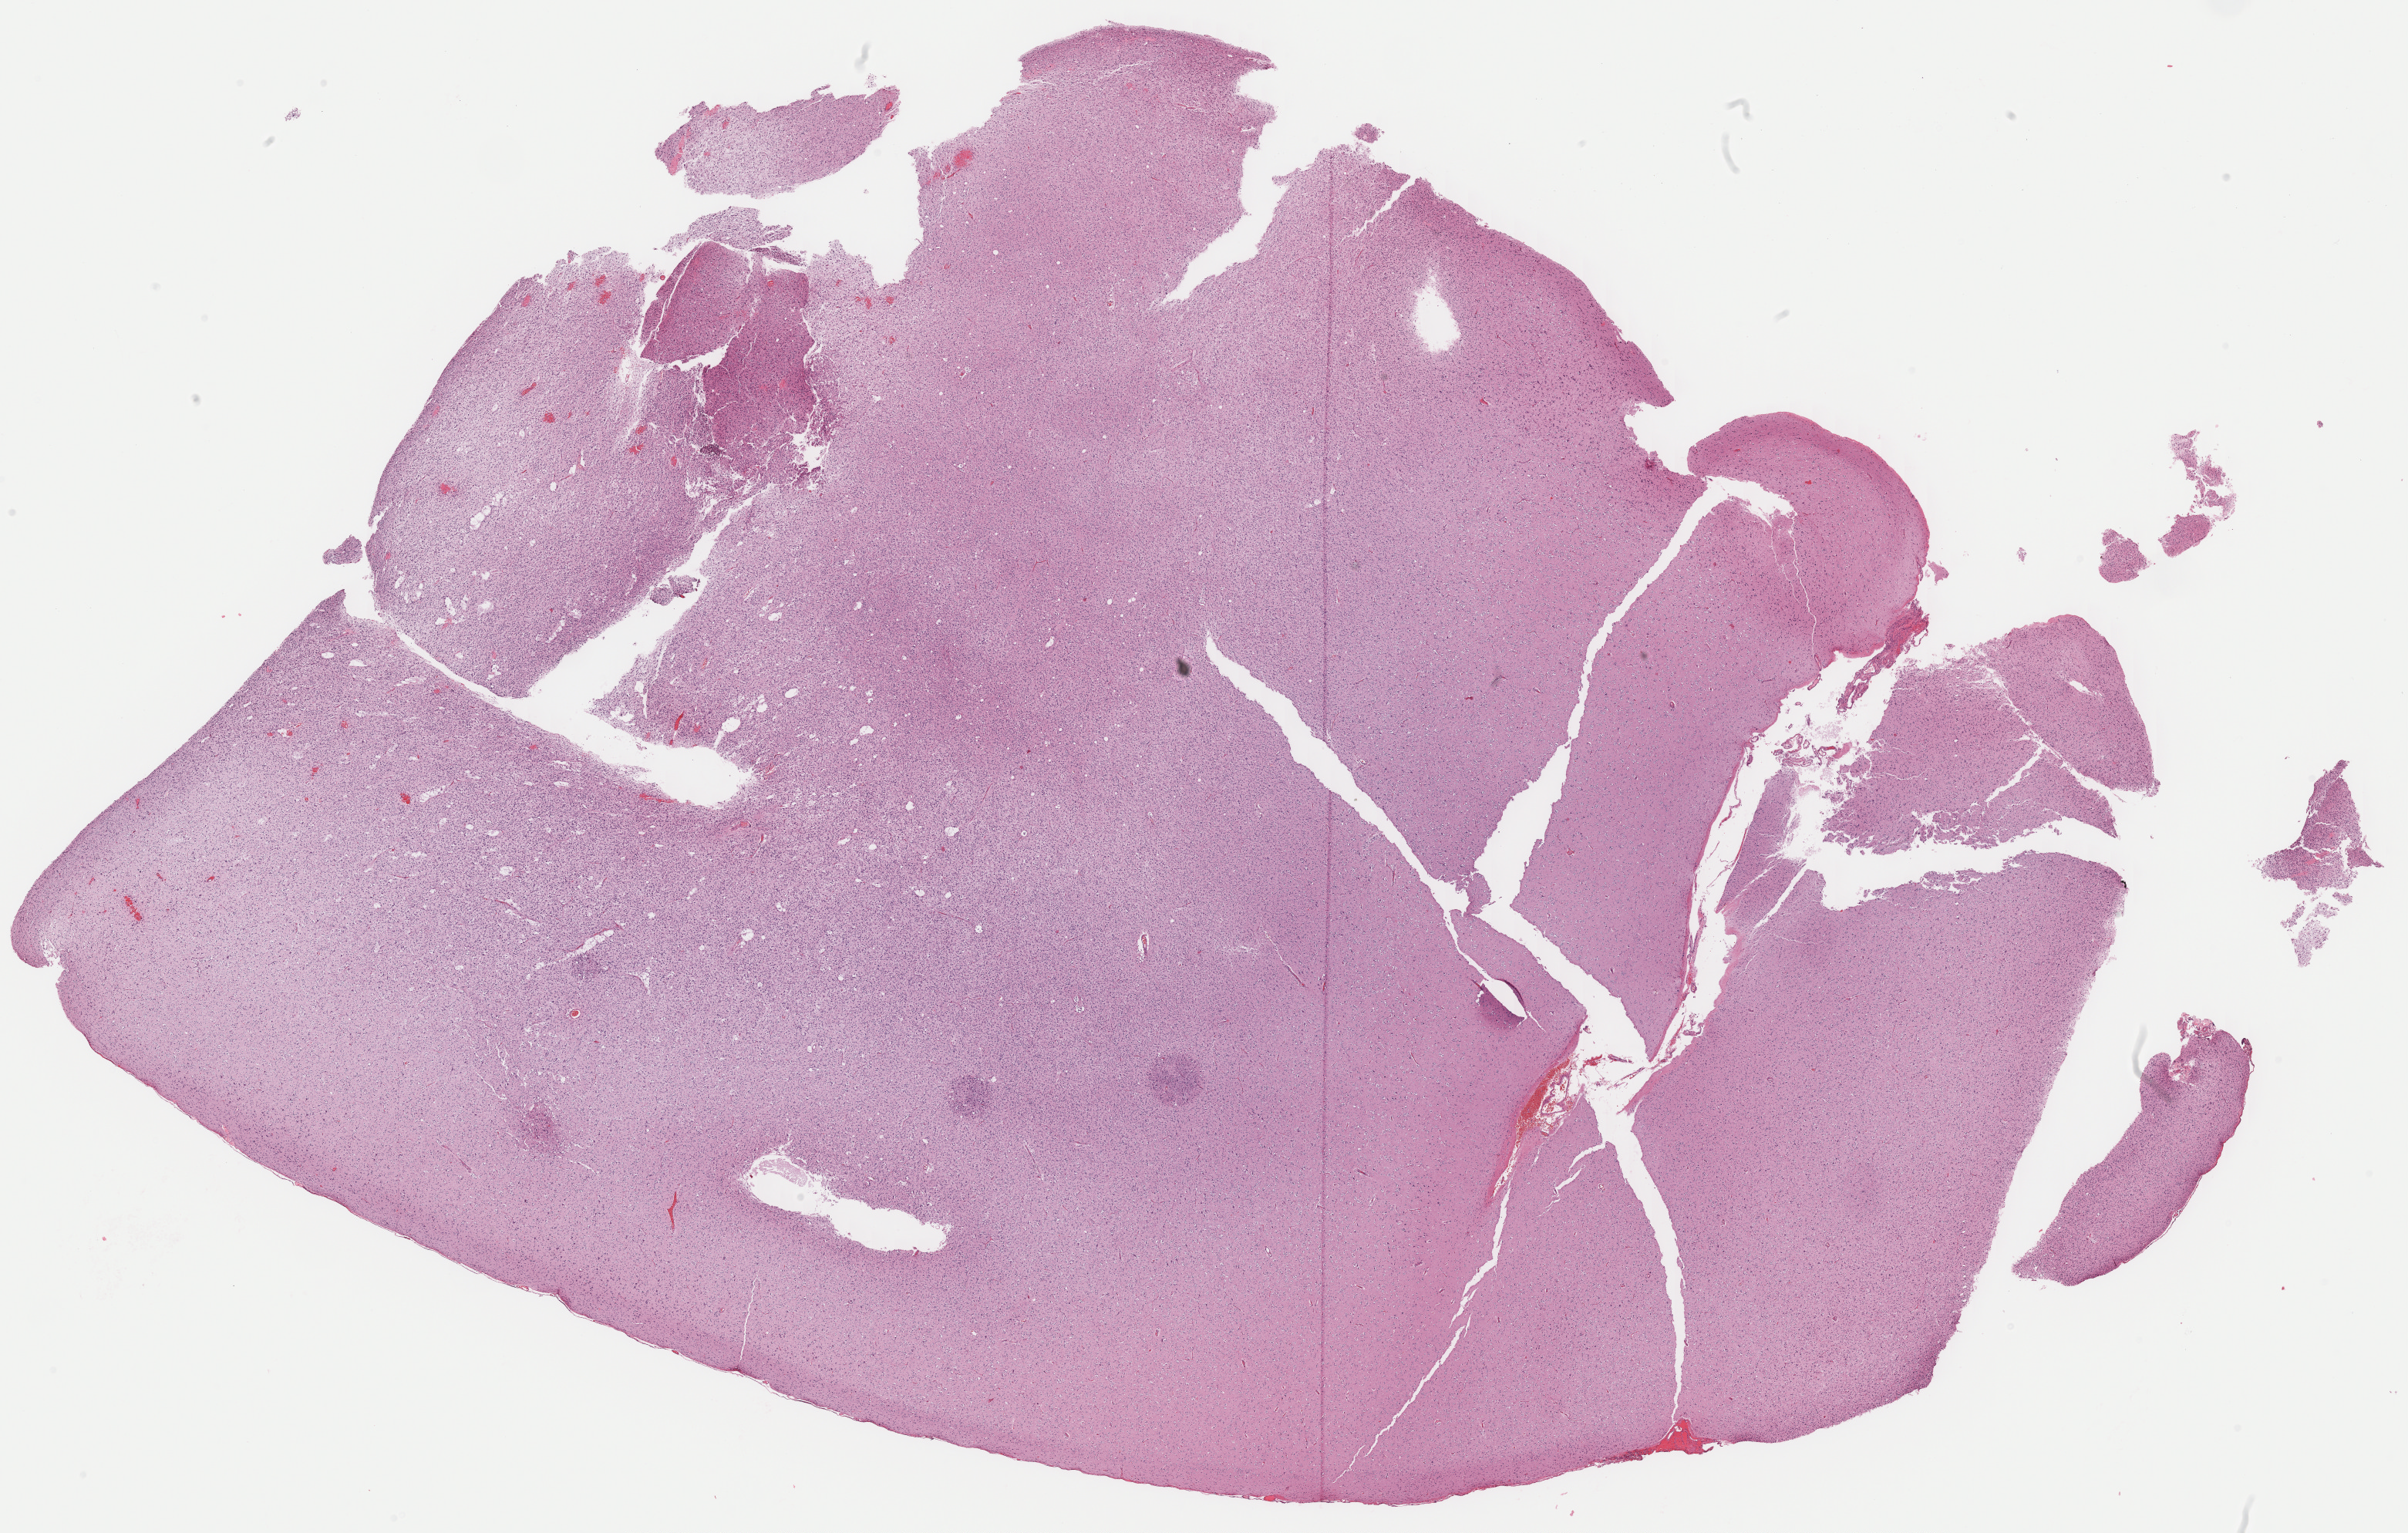
H&E-stained whole-slide image — shown as a low-resolution overview of the whole scanned area (about 24.6 x 15.7 mm); FFPE section; sample: primary tumour, brain. Female patient; age at initial diagnosis 33 years. Histologic grade: G2 (moderately differentiated).
Pathologic diagnosis: Mixed glioma (temporal lobe).